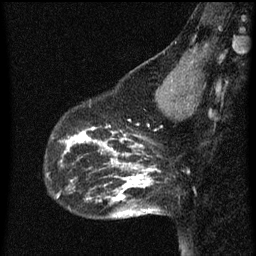
Breast MRI (dynamic contrast-enhanced), one sagittal slice; position 18 of 60 along the scan axis; dynamic contrast-enhanced series, image 2 of 3 at this slice position (ordered by acquisition); 1.5 T; TE 4.2 ms, TR 8 ms; 256 × 256 image matrix, field of view 180 × 180 mm. Patient: female, 43 years.
Annotated regions visible in this slice (semi-automatically segmented with operator editing):
- analysis volume of interest (the breast-tissue region the enhancement analysis was run in; not a lesion): bounding box [x1, y1, x2, y2] px = [53, 104, 101, 155]
- tumour enhancement mask (voxels above the 70 % enhancement threshold inside the analysis volume of interest): [61, 128, 101, 155]